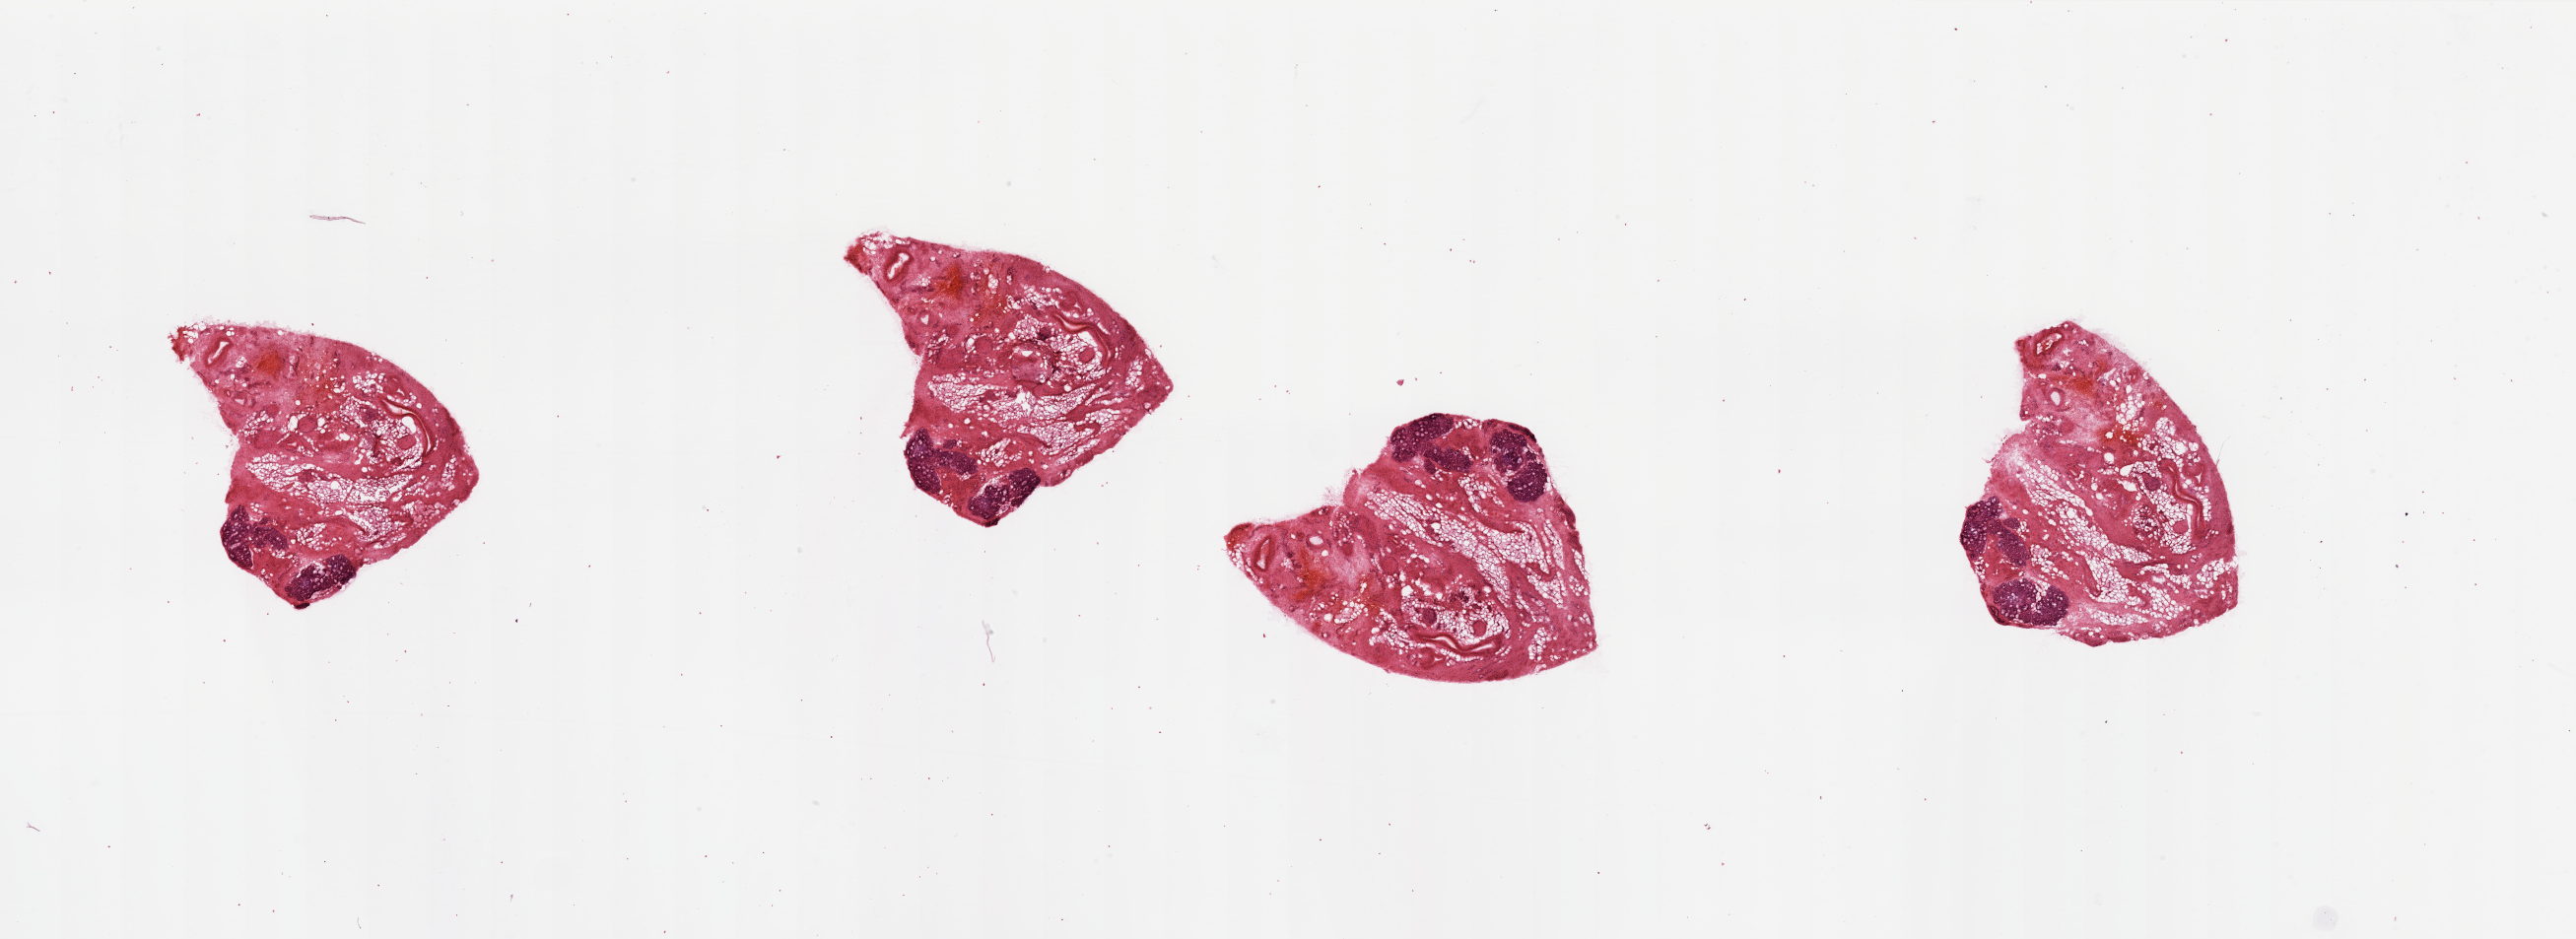
H&E-stained whole-slide image, low-resolution overview of the scanned area, about 41.3 x 15.1 mm (from a 20x scan), head and neck, tissue type not recorded. 67-year-old male patient.
Patient diagnosis: Squamous cell carcinoma, NOS.